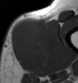
MRI of an extremity soft-tissue mass, one axial slice. Position 14 of 43 along the scan axis. MR volume resampled by the dataset authors to the PET/CT grid (not the native acquisition matrix). 3.27 mm slice thickness. 78 × 83 image matrix, field of view 76 × 81 mm. Male patient. From the clinical record (not read from this slice): histological type: pleiomorphic leiomyosarcoma; grade: high; site of the primary tumour: left thigh.
Structures marked on this image (expert contour drawn on MRI and transferred to this co-registered scan by the dataset authors):
- gross tumour volume including surrounding oedema: bounding box (x1, y1, x2, y2) in pixels: (11, 19, 58, 66)
- gross tumour volume (mass): (11, 19, 55, 66)